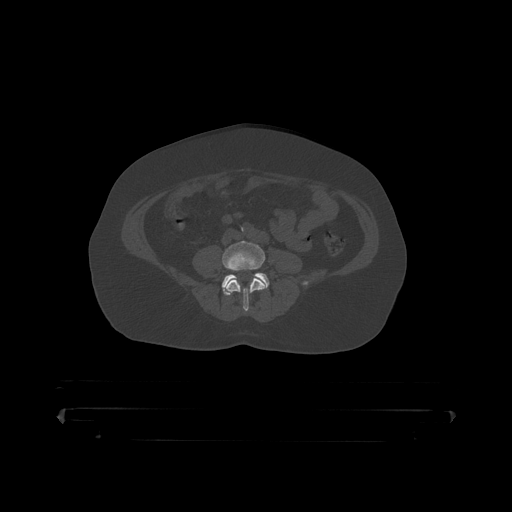
CT including the spine, one axial slice. 120 kVp. Bone window (W 1800 / L 400 HU). 1.25 mm slice thickness. 512 × 512 image matrix, field of view 650 × 650 mm. Patient: male, 60 years. Case-level facts recorded for this patient, not image findings: primary cancer: prostate.
Structures marked on this image (semi-automatic segmentation, software-assisted and operator-edited):
- L4 vertebra: bounding box (x1, y1, x2, y2) in pixels: (223, 242, 266, 312)
- L5 vertebra: (222, 273, 270, 295)